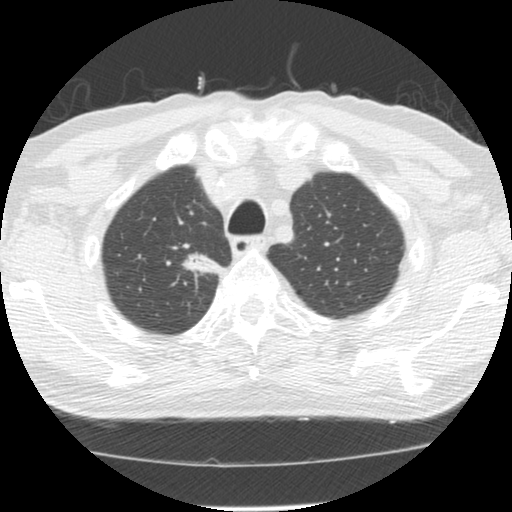
Low-dose screening chest CT, one axial slice; slice 112 of 139 in the series (ordered by position); reconstruction kernel STANDARD; lung window (W 1500 / L -600 HU); 2.5 mm slice thickness; 512 × 512 image matrix.
Annotated regions visible in this slice (outlined manually by an expert reader):
- lesion 1 (tumor, upper lobe of right lung): bounding box [x1, y1, x2, y2] px = [181, 252, 221, 278]